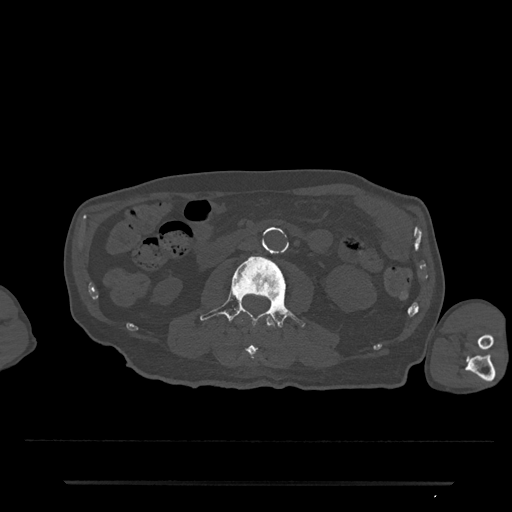
CT including the spine, one axial slice; position 5 of 797 along the scan axis; 120 kVp; bone window (W 1800 / L 400 HU); 0.5 mm slice thickness; 512 × 512 image matrix, field of view 427 × 427 mm. Male patient, age 74 years. Case-level facts recorded for this patient, not image findings: primary cancer: prostate.
Annotated regions visible in this slice (semi-automatic segmentation, software-assisted and operator-edited):
- L2 vertebra: bounding box [x1, y1, x2, y2] px = [239, 315, 277, 361]
- L3 vertebra: [200, 255, 306, 328]